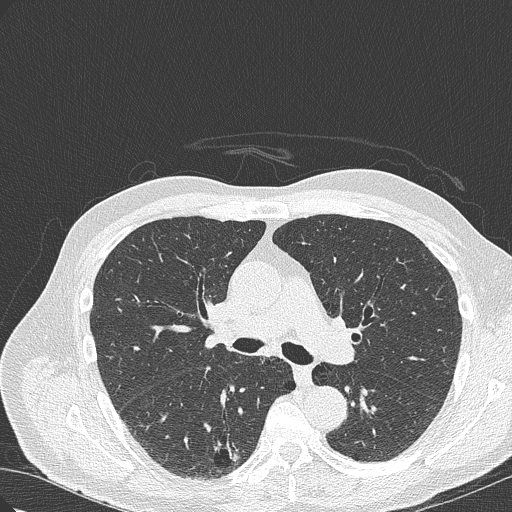
Low-dose screening chest CT, axial slice, first (baseline) screen, lung window (W 1500 / L -600 HU), slice 123 of 322 in the series. Male participant, aged 70 years at enrolment. Current smoker at enrolment.
- Expert reader's lesion annotation, box from (x=200, y=419) to (x=264, y=471) px.
- The screening reader recorded 4 non-calcified nodules or masses ≥4 mm on this exam; which of them this box marks is not recorded.
- Participant outcome: lung cancer diagnosed 978 days after this screen (after the third annual screen) — bronchiolo-alveolar adenocarcinoma, NOS, right lower lobe, poorly differentiated (G3), stage IB (AJCC 6th edition), 30 mm at pathology.